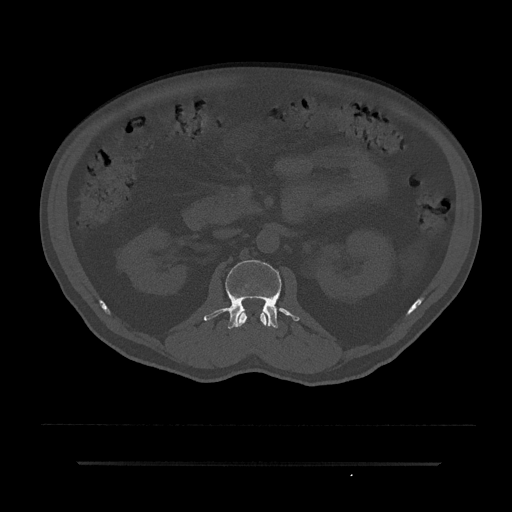
CT including the spine, one axial slice. 120 kVp. Bone window (W 1800 / L 400 HU). 0.5 mm slice thickness. 512 × 512 image matrix, field of view 464 × 464 mm. Male patient, age 59 years. From the clinical record (not read from this slice): primary cancer: bile ducts; vertebrae with lytic lesions (as recorded): T10.
Outlined on this slice (semi-automatic segmentation, software-assisted and operator-edited):
- L1 vertebra: bounding box (x1, y1, x2, y2) in pixels: (238, 311, 267, 327)
- L2 vertebra: (204, 260, 299, 329)